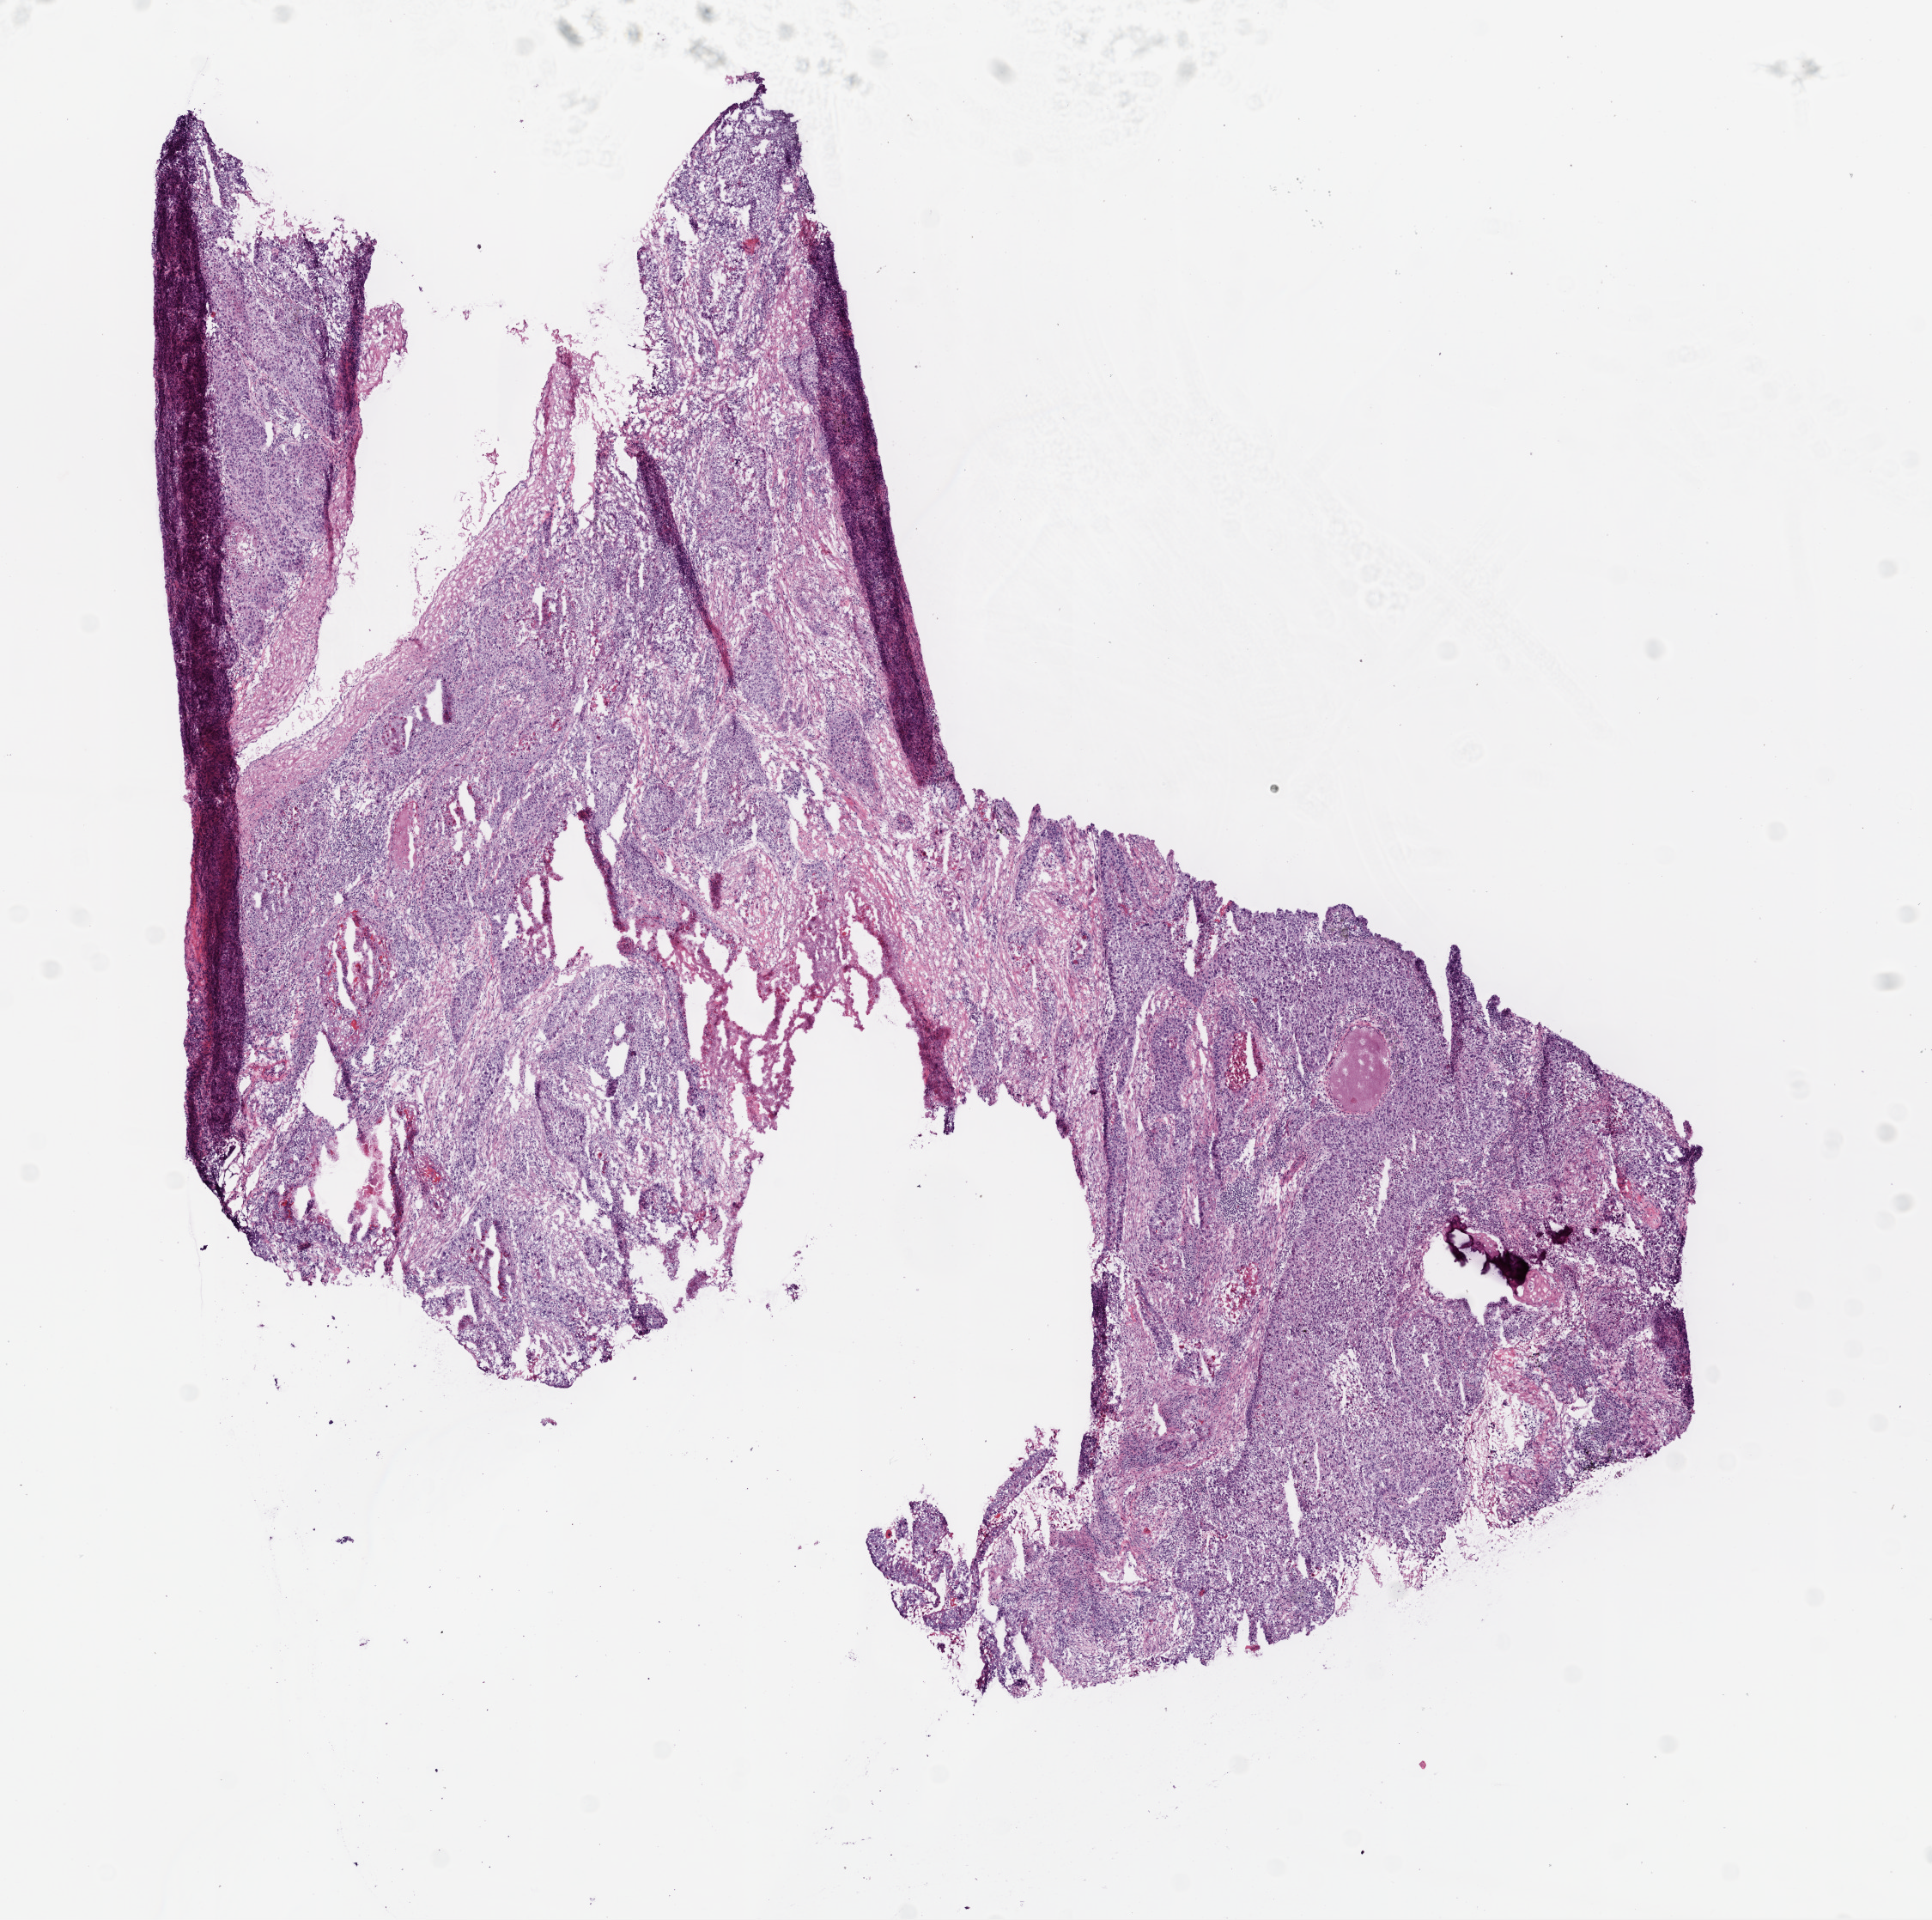
H&E whole-slide image, shown as a low-resolution overview of the whole scanned area (about 9.0 x 9.0 mm, acquisition: 20x scan); frozen section from the bottom of the tissue portion; sample: primary tumour, lung. Patient: male, age at initial diagnosis 66 years. Pathologist review of this section (percent, as recorded): tumour cells 68%, tumour nuclei 70%, normal cells 2%, stromal cells 15%, necrosis 15%.
- laterality: left
- AJCC pathologic stage: IB (6th edition)
- pathologic diagnosis: Squamous cell carcinoma, NOS (upper lobe, lung)